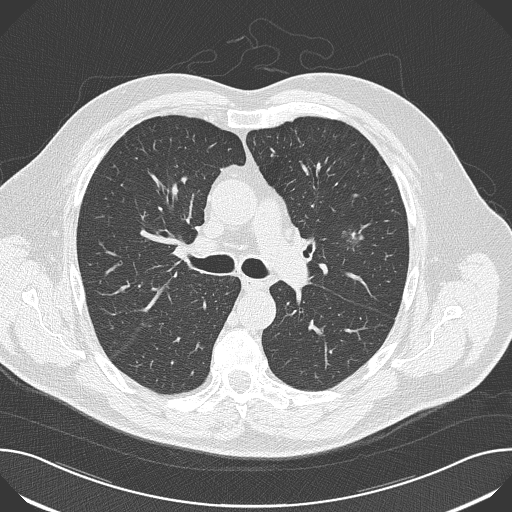
Axial slice from a low-dose chest CT screening exam. First (baseline) screen. Lung window (W 1500 / L -600 HU). Slice 65 of 174 in the series. Male participant, aged 65 years at enrolment. Former smoker at enrolment.
- Expert reader's lesion annotation, bounding box [x1, y1, x2, y2] px = [333, 219, 373, 259].
- The screening reader recorded 5 non-calcified nodules or masses ≥4 mm on this exam (left upper lobe, left upper lobe, left upper lobe, right upper lobe, right middle lobe); which of them this box marks is not recorded.
- Official screen result: positive, change unspecified: nodule(s) >= 4 mm or enlarging nodule(s), mass(es), or other non-specific abnormalities suspicious for lung cancer.
- Participant outcome: lung cancer diagnosed 52 days after this screen — adenocarcinoma, NOS, left upper lobe, moderately differentiated (G2), stage IA (AJCC 6th edition), 10 mm at pathology.